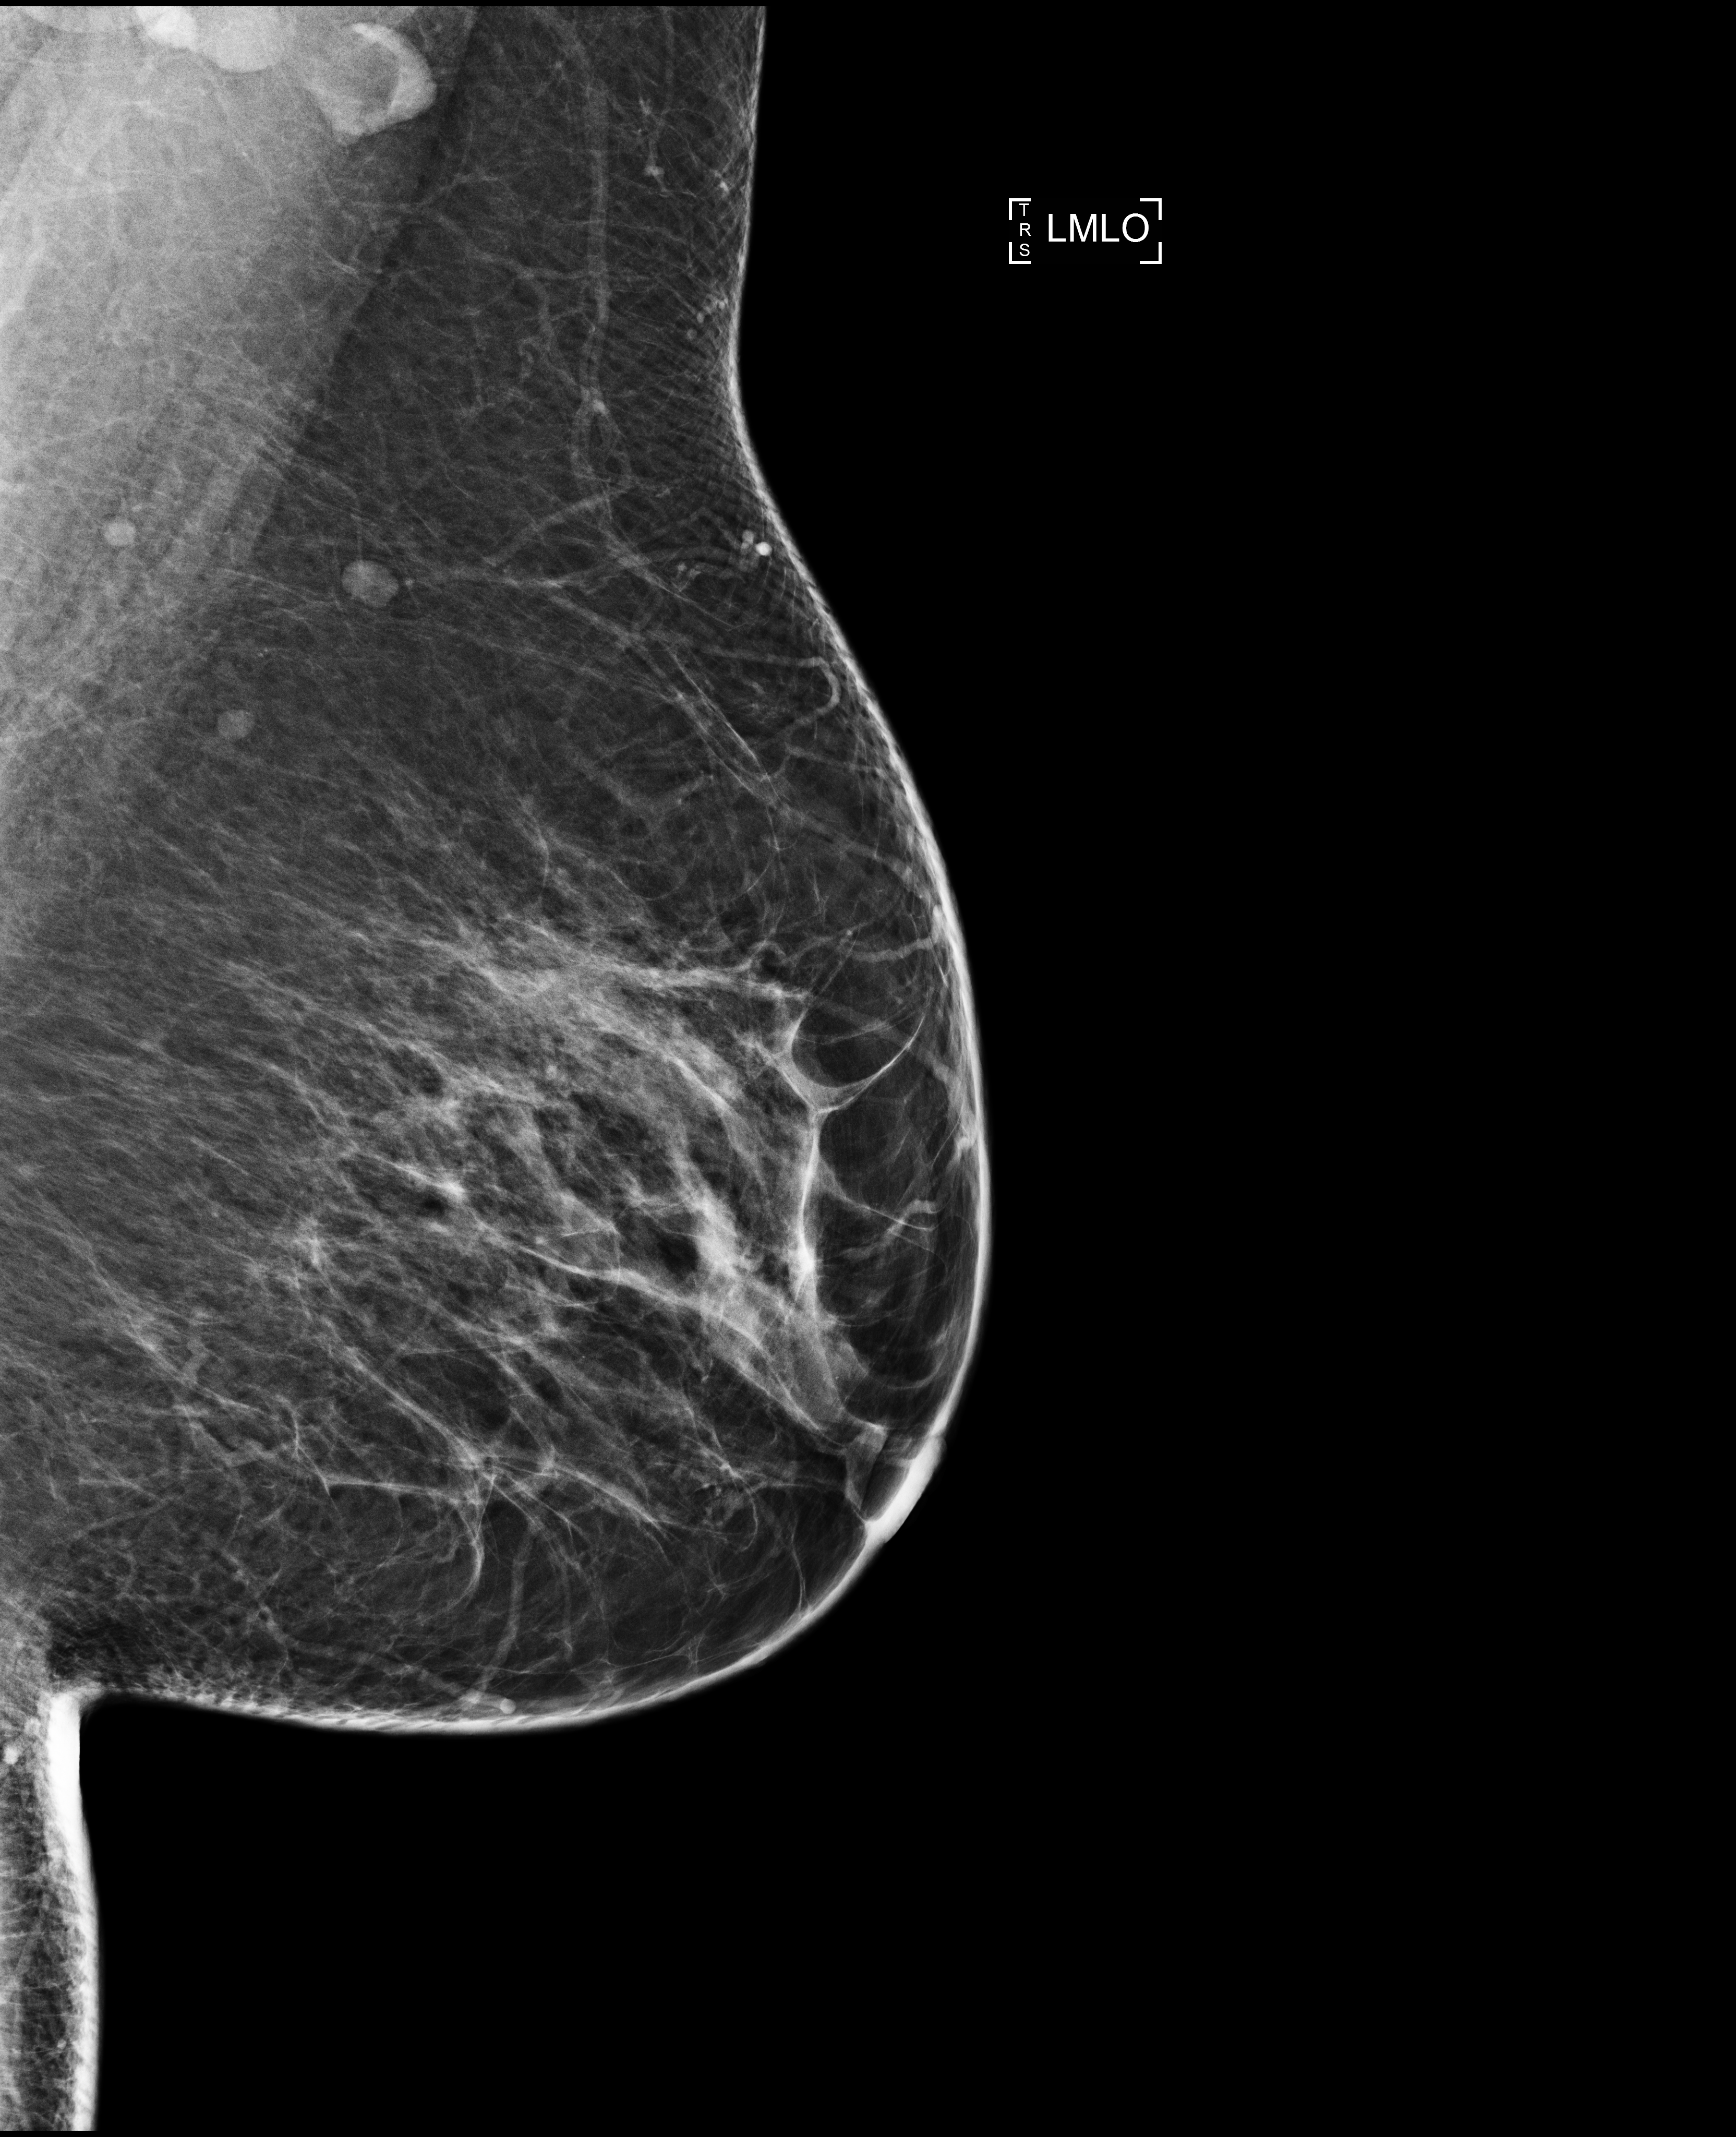
Annual screening mammography examination; compressed breast thickness 66 mm. Female patient, age 47 years.
Image type: full-field digital mammogram. Breast: left. Projection: medio-lateral oblique projection.